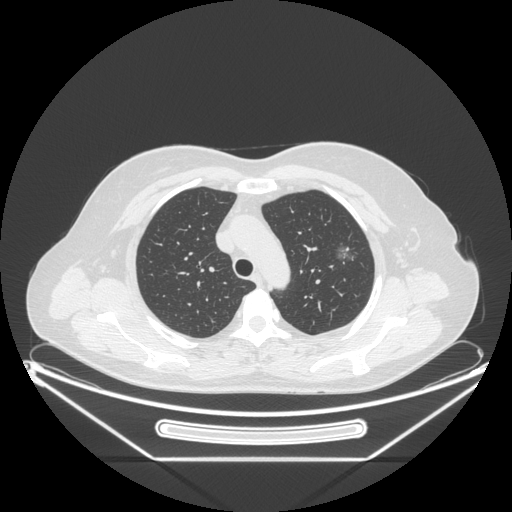
Chest CT, one axial slice; slice 166 of 226 in the series (ordered by position); reconstruction kernel STANDARD; lung window (W 1500 / L -600 HU); 1.25 mm slice thickness; 512 × 512 image matrix. Patient: female, 54 years. Case-level facts recorded for this patient, not image findings: clinical TNM (as recorded): T1c N0 M0; histopathological grade: G1.
Structures marked on this image (rectangle marked by the reading radiologist):
- lung tumour (recorded histology: adenocarcinoma): bounding box (x1, y1, x2, y2) in pixels: (331, 237, 365, 276)